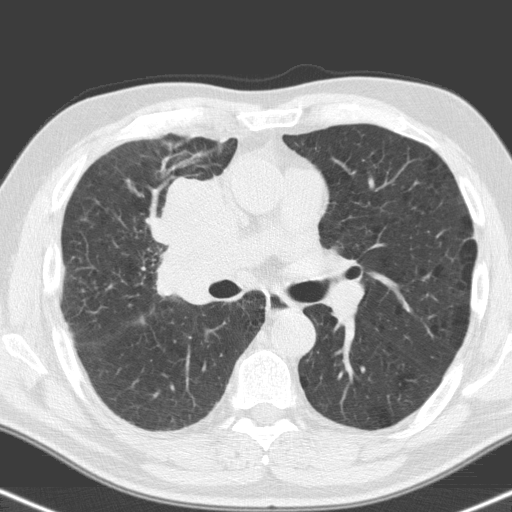
Low-dose screening chest CT, one axial slice; position 94 of 160 along the scan axis; lung window (W 1500 / L -600 HU); 3.2 mm slice thickness; 512 × 512 image matrix.
Outlined on this slice (manually delineated by an expert):
- lesion 1 (tumor, hilum of right lung): box from (x=158, y=177) to (x=251, y=304) px